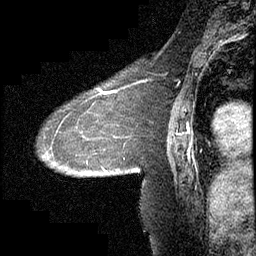
Breast MRI (dynamic contrast-enhanced), one sagittal slice; dynamic contrast-enhanced study with each time point stored as its own series, time point 2 of 4 at this slice position (early post-contrast, ordered by acquisition time); 1.5 T; TE 4.2 ms, TR 6.7 ms; 3 mm slice thickness; 256 × 256 image matrix. Female patient, age 63 years. Case-level facts recorded for this patient, not image findings: setting: breast cancer imaged before/during neoadjuvant chemotherapy; receptor status: triple-negative.
Outlined on this slice (semi-automatically segmented with operator editing):
- analysis volume of interest (the breast-tissue region the enhancement analysis was run in; not a lesion): bounding box [x1, y1, x2, y2] px = [38, 90, 140, 178]
- tumour enhancement mask (voxels above the 70 % enhancement threshold inside the analysis volume of interest): [99, 90, 125, 172]